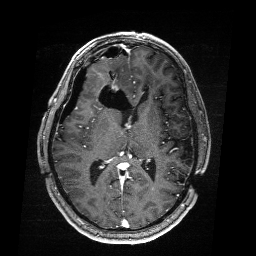
Brain MRI from a brain-tumour surgery series, one axial slice; position 101 of 176 along the scan axis; T1-weighted post-contrast; 256 × 256 image matrix, field of view 256 × 256 mm. Case-level facts recorded for this patient, not image findings: histopathology: Astrocytoma; WHO grade: 4; IDH mutation: yes.
Annotated regions visible in this slice (outlined manually by an expert reader):
- residual tumour: bounding box (x1, y1, x2, y2) in pixels: (96, 82, 117, 89)